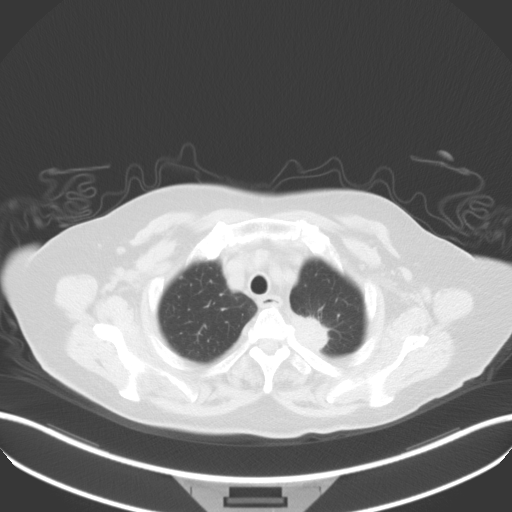
Chest CT, one axial slice. Slice 35 of 42 in the series (ordered by position). Reconstruction kernel B31f. 100 kVp. Lung window (W 1500 / L -600 HU). 512 × 512 image matrix, field of view 400 × 400 mm. Female patient, age 81 years. Case-level facts recorded for this patient, not image findings: clinical TNM (as recorded): T2a N0 M0.
Outlined on this slice (bounding box drawn by a radiologist):
- lung tumour (recorded histology: adenocarcinoma): box from (x=290, y=308) to (x=337, y=355) px